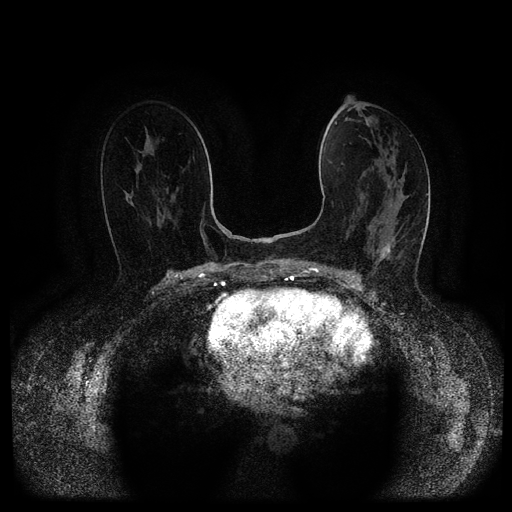
Breast MRI (dynamic contrast-enhanced, multi-phase), one axial slice. Position 54 of 116 along the scan axis. Dynamic contrast-enhanced series, time point 2 of 5 at this slice position (early post-contrast). 1.5 T. TE 2.6 ms, TR 5.4 ms. 512 × 512 image matrix. Female patient, age 61 years.
Outlined on this slice (semi-automatically segmented with operator editing):
- breast lesion (labelled 'tumour' in the annotation; benign lesions carry a separate 'benign' label): bounding box <378,240,393,264> (left, top, right, bottom; pixels)